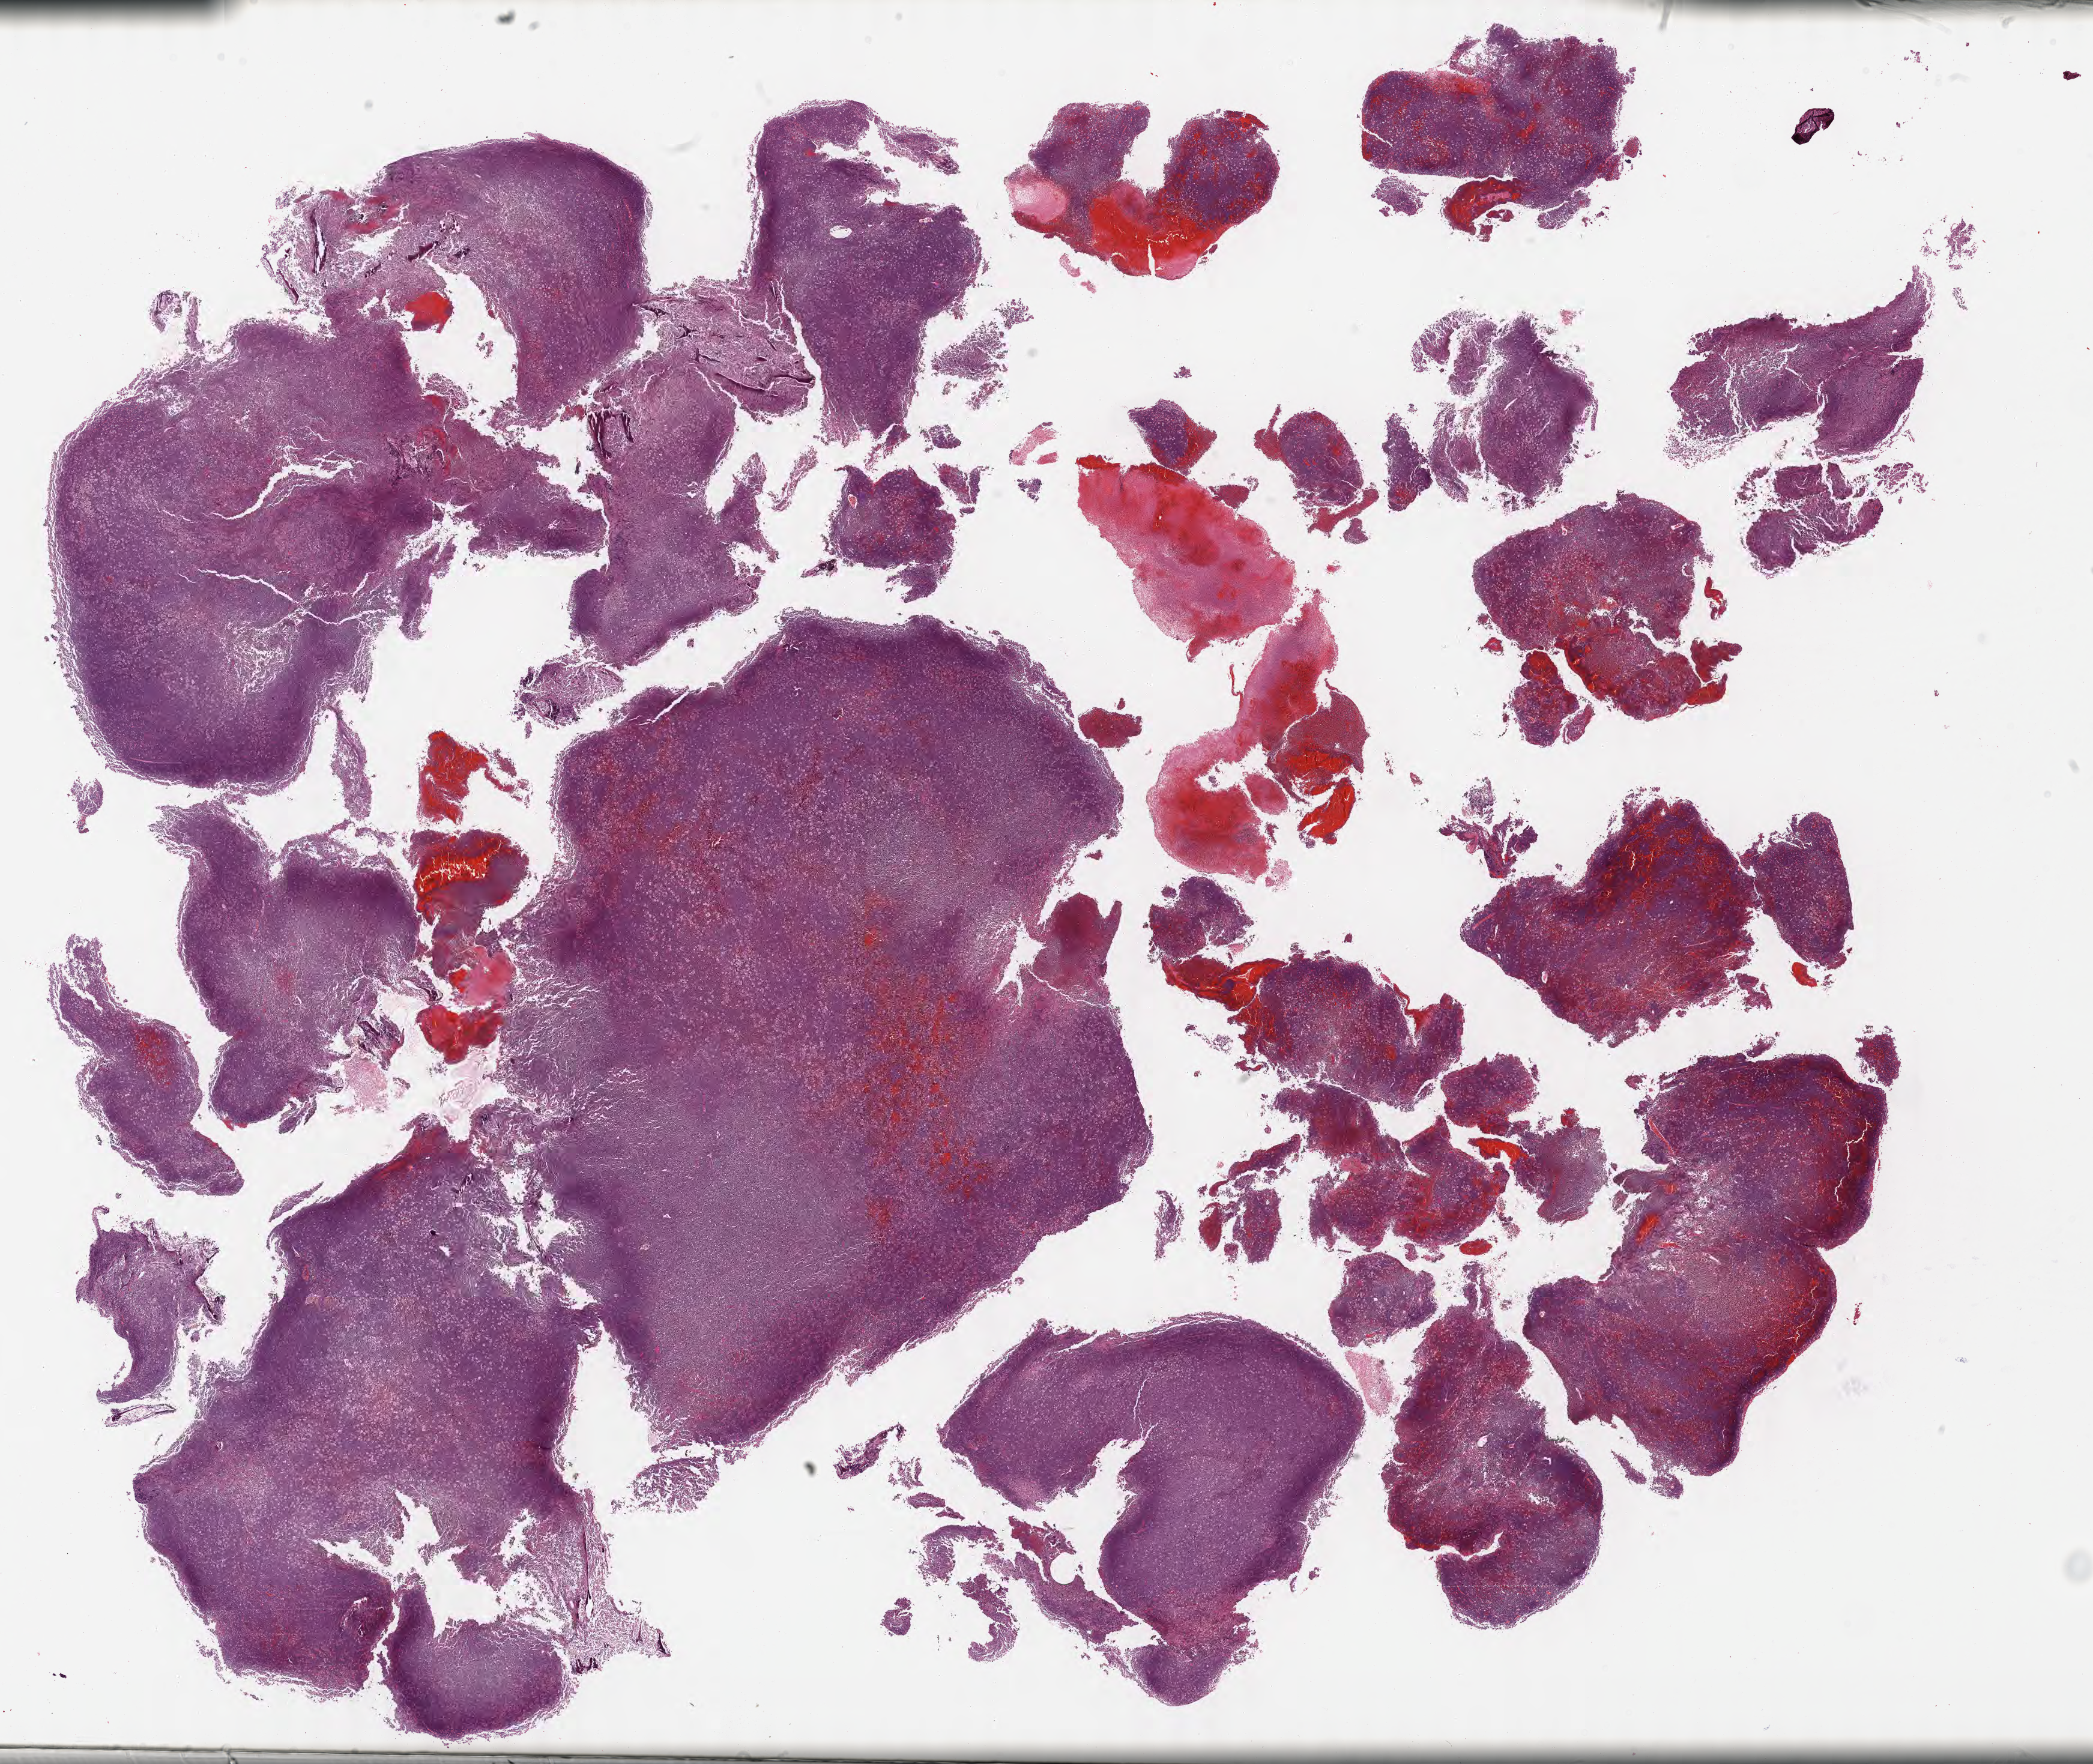
Hematoxylin and eosin (H&E) whole-slide image, whole scanned area (about 28.2 x 23.7 mm) shown as a low-resolution overview, FFPE section, specimen: primary tumor. Female patient; age at initial diagnosis 6 years. Pathologist review of this section (percent, as recorded): tumor cells 95%, tumor nuclei 95%, stromal cells 0%, necrosis 5%, normal cells 0%. Infiltration values recorded for this section: lymphocyte infiltration 20%, monocyte infiltration 50%, neutrophil infiltration 10%.
* diagnosis: Burkitt lymphoma, NOS
* Ann Arbor stage (patient): Stage IV